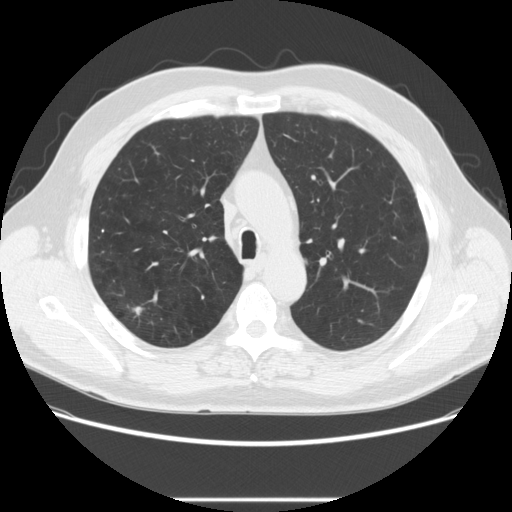
Axial slice from a low-dose chest CT screening exam, baseline annual screen, lung window (W 1500 / L -600 HU), 2.5 mm slice thickness, slice 79 of 270 in the series. Male participant, aged 64 years at enrolment. Former smoker at enrolment.
Expert-annotated lung lesion, bounding box [x1, y1, x2, y2] px = [116, 298, 152, 326]. The screening reader recorded 2 non-calcified nodules or masses ≥4 mm on this exam; which of them this box marks is not recorded. Official screen result: positive, change unspecified: nodule(s) >= 4 mm or enlarging nodule(s), mass(es), or other non-specific abnormalities suspicious for lung cancer.